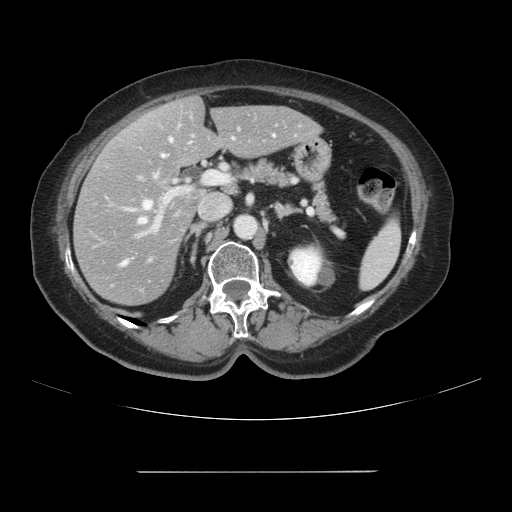
Contrast-enhanced abdominal CT, one axial slice. Slice 53 of 111 in the series (ordered by position). 120 kVp. Intravenous contrast given. Soft-tissue window (W 400 / L 40 HU). 2.5 mm slice thickness. 512 × 512 image matrix, field of view 400 × 400 mm. Female patient, age 74 years. Case-level facts recorded for this patient, not image findings: diagnosis: colorectal cancer liver metastases, imaged before liver resection; multiple liver metastases: yes; largest metastasis: 1.1 cm.
Annotated regions visible in this slice (outlined manually by an expert reader):
- hepatic veins: box from (x=123, y=139) to (x=172, y=265) px
- liver: (x=75, y=98)–(x=319, y=305)
- planned liver remnant (the part of the liver to remain after resection): (x=144, y=98)–(x=319, y=166)
- portal vein (with intrahepatic branches): (x=135, y=124)–(x=302, y=238)